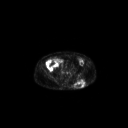
FDG PET of an extremity soft-tissue mass (from a PET/CT study), one axial slice; position 88 of 267 along the scan axis; 3.27 mm slice thickness; 128 × 128 image matrix, field of view 700 × 700 mm. Patient: male, 69 years. From the clinical record (not read from this slice): histological type: leiomyosarcoma; grade: intermediate; site of the primary tumour: left pelvis.
Outlined on this slice (expert contour drawn on MRI and transferred to this co-registered scan by the dataset authors):
- gross tumour volume (mass): bounding box [x1, y1, x2, y2] px = [74, 79, 86, 88]